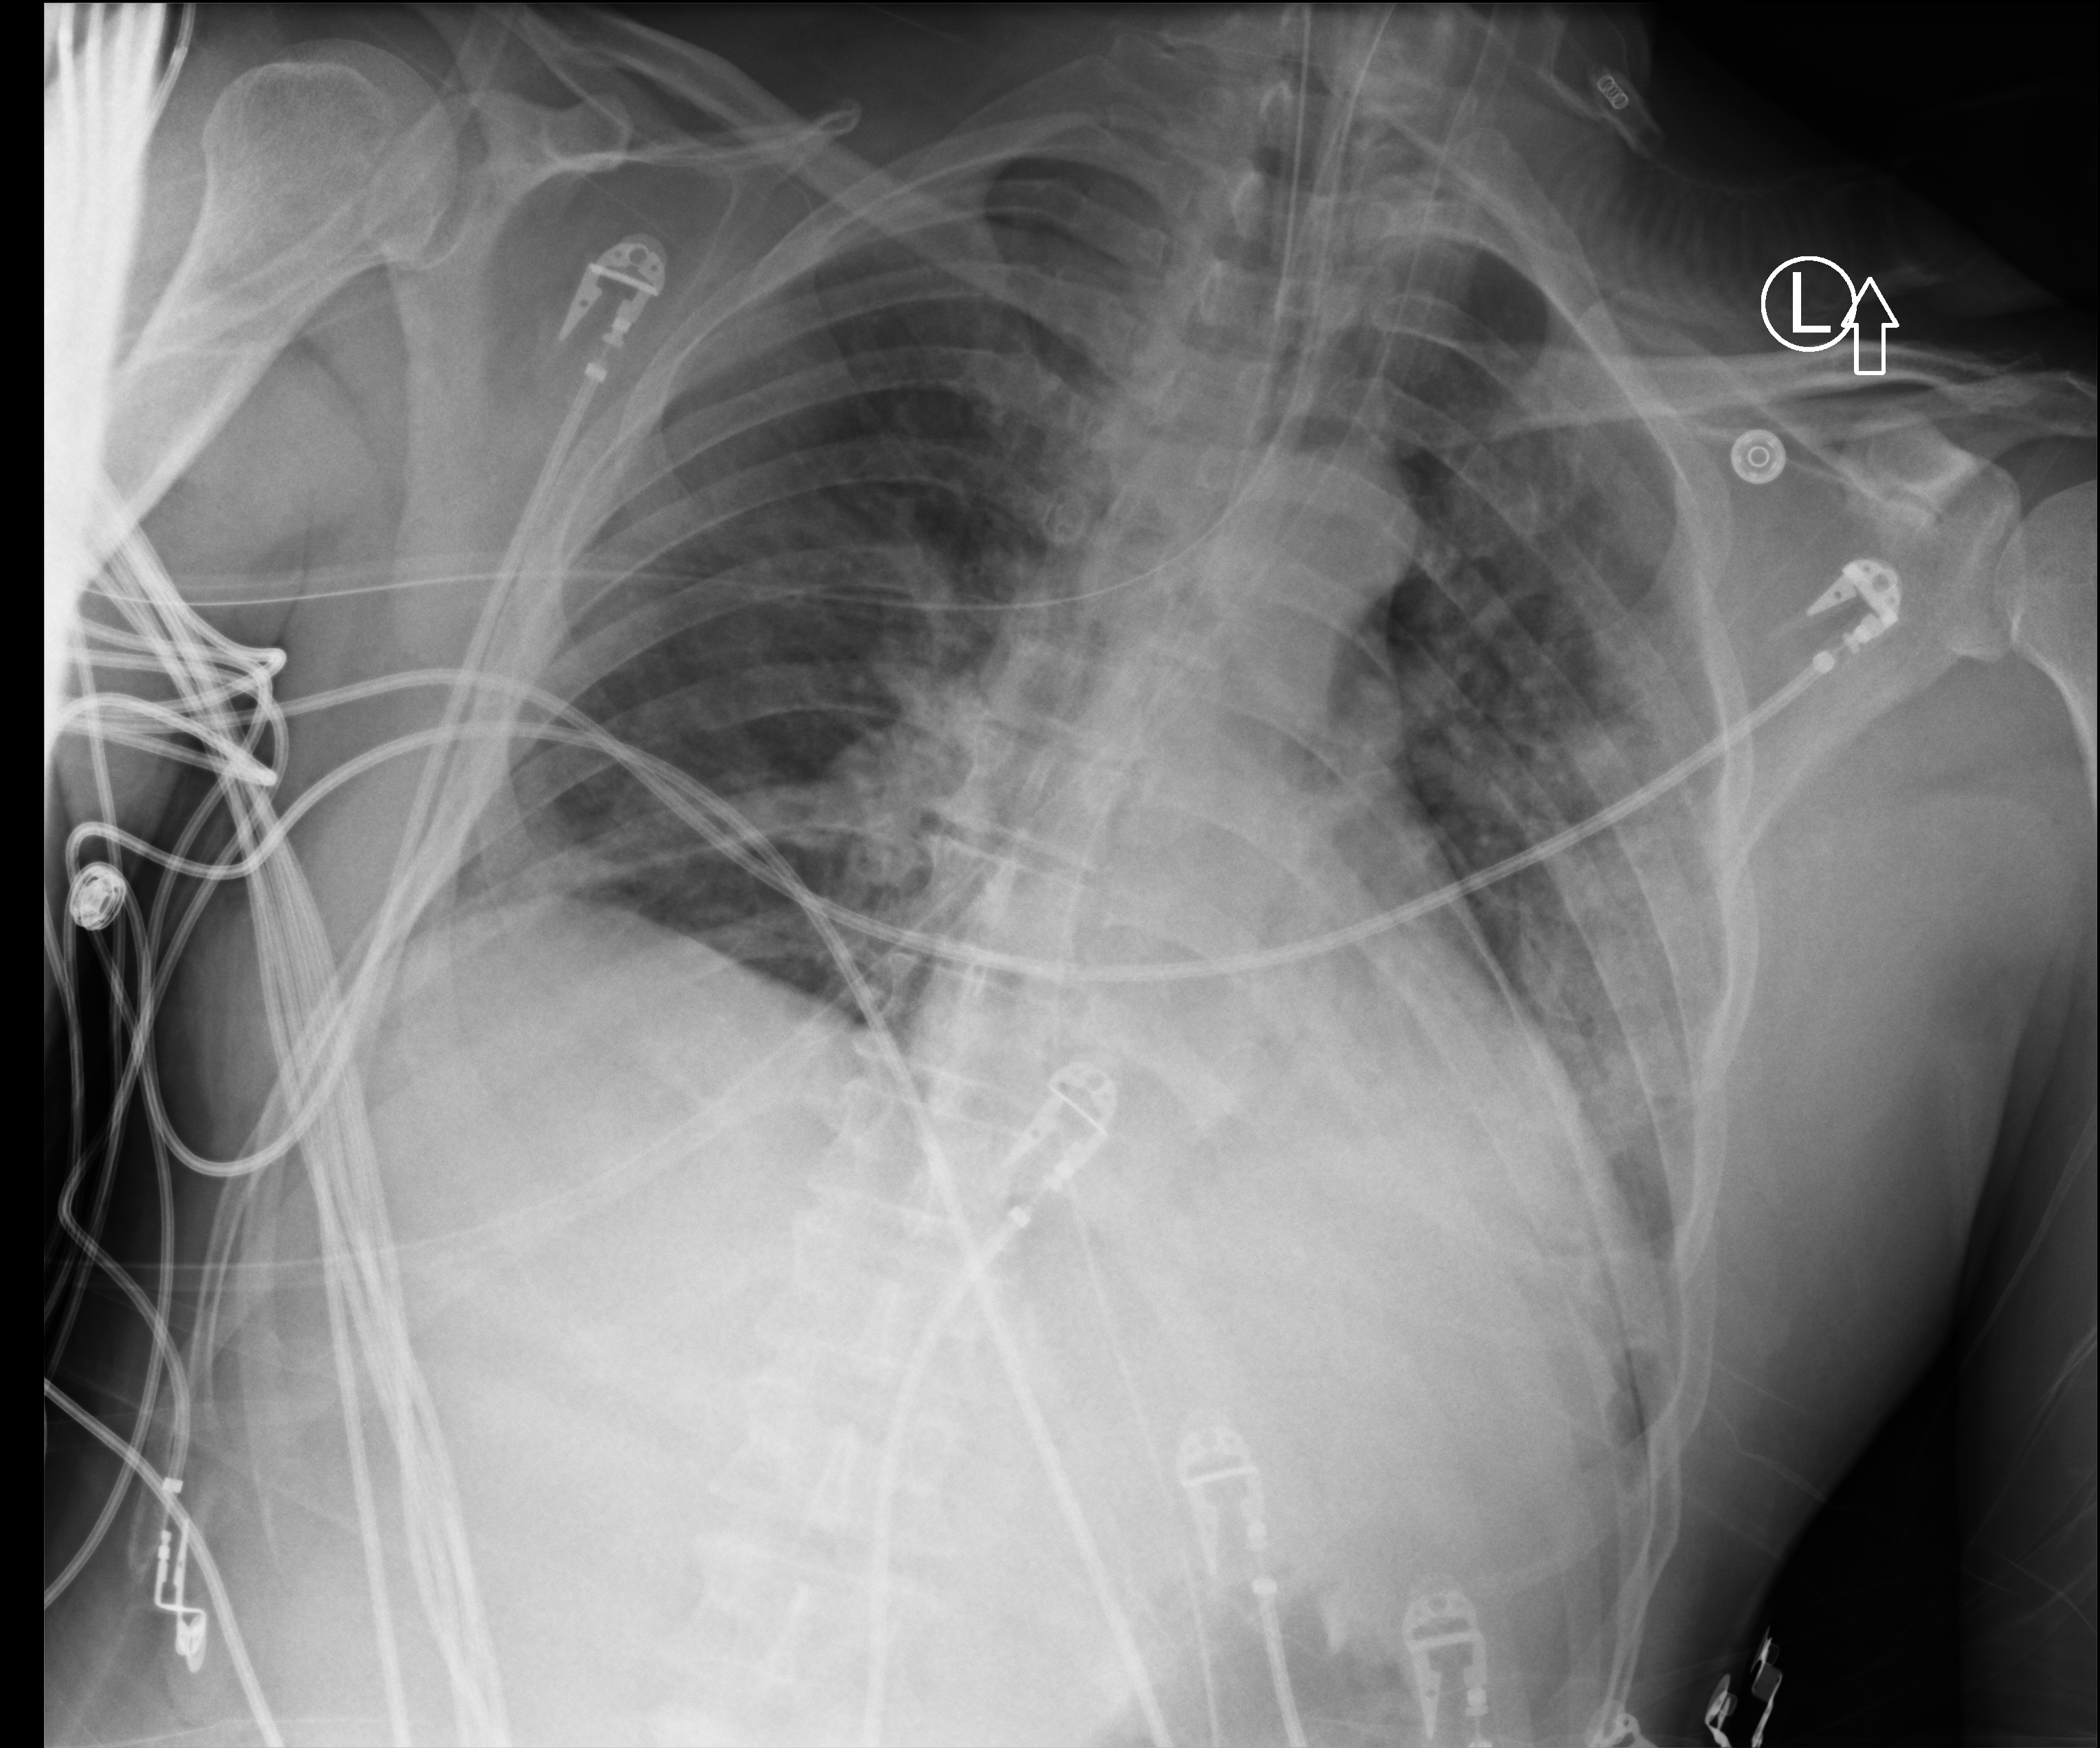
Bedside chest radiograph (computed radiography); anteroposterior (AP) projection. Male patient hospitalised with COVID-19, age 18–59 years.
From the hospital-stay record, not from the radiograph (when in the stay this image was taken is not recorded): length of hospital stay: 14 days; smoking status (admission record): never; admitted to intensive care during this hospital stay: yes.